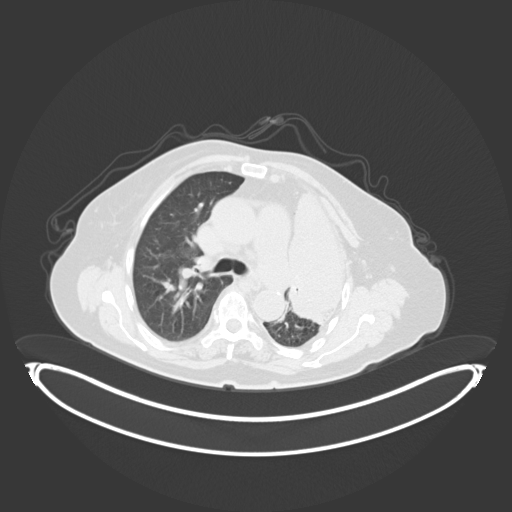
Chest CT, one axial slice. Slice 210 of 284 in the series (ordered by position). Reconstruction kernel B30f. 120 kVp. Lung window (W 1500 / L -600 HU). 3 mm slice thickness. 512 × 512 image matrix, field of view 500 × 500 mm. Patient: female, 75 years. Case-level facts recorded for this patient, not image findings: clinical TNM (as recorded): T3 N3 M1.
Structures marked on this image (bounding box drawn by a radiologist):
- lung tumour (recorded histology: adenocarcinoma): box from (x=285, y=187) to (x=355, y=330) px